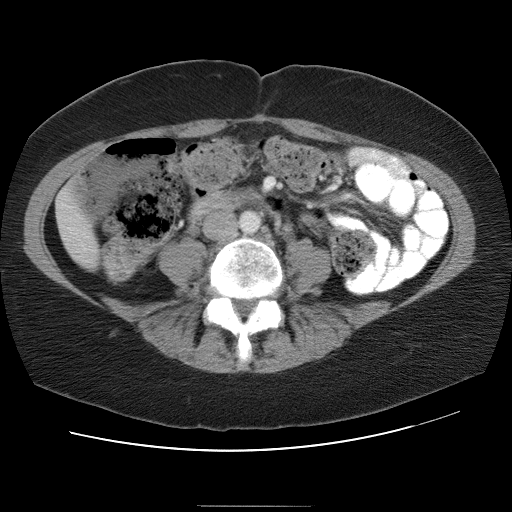
Contrast-enhanced abdominal CT, one axial slice; slice 4 of 30 in the series (ordered by position); reconstruction kernel STANDARD; 120 kVp; intravenous contrast given; soft-tissue window (W 400 / L 40 HU); 7.5 mm slice thickness; 512 × 512 image matrix, field of view 376 × 376 mm. Female patient, age 52 years. Case-level facts recorded for this patient, not image findings: diagnosis: colorectal cancer liver metastases, imaged before liver resection; multiple liver metastases: no; largest metastasis: 3 cm; disease in both lobes: yes.
Outlined on this slice (expert manual segmentation):
- liver: bounding box [x1, y1, x2, y2] px = [55, 193, 102, 268]